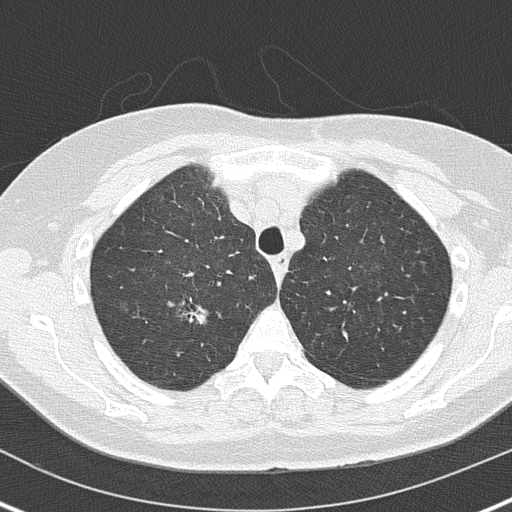
Low-dose screening chest CT, axial slice. First (baseline) screen. Lung window (W 1500 / L -600 HU). 120 kVp. Slice 36 of 162 in the series. 512 × 512 image matrix. Female participant, aged 61 years at enrolment. Current smoker at enrolment.
• Expert-annotated lung lesion, bounding box [x1, y1, x2, y2] px = [180, 296, 219, 330].
• Screening reader's record for this exam (one nodule recorded; not confirmed to be the boxed lesion): non-calcified nodule or mass ≥4 mm, right upper lobe, 8 × 5 mm, smooth margins, soft tissue attenuation.
• Official screen result: positive, change unspecified: nodule(s) >= 4 mm or enlarging nodule(s), mass(es), or other non-specific abnormalities suspicious for lung cancer.
• Lung cancer was diagnosed 438 days after this screen (after the second annual screen): adenocarcinoma, NOS, right upper lobe, moderately differentiated (G2), stage IA (AJCC 6th edition), 20 mm at pathology.